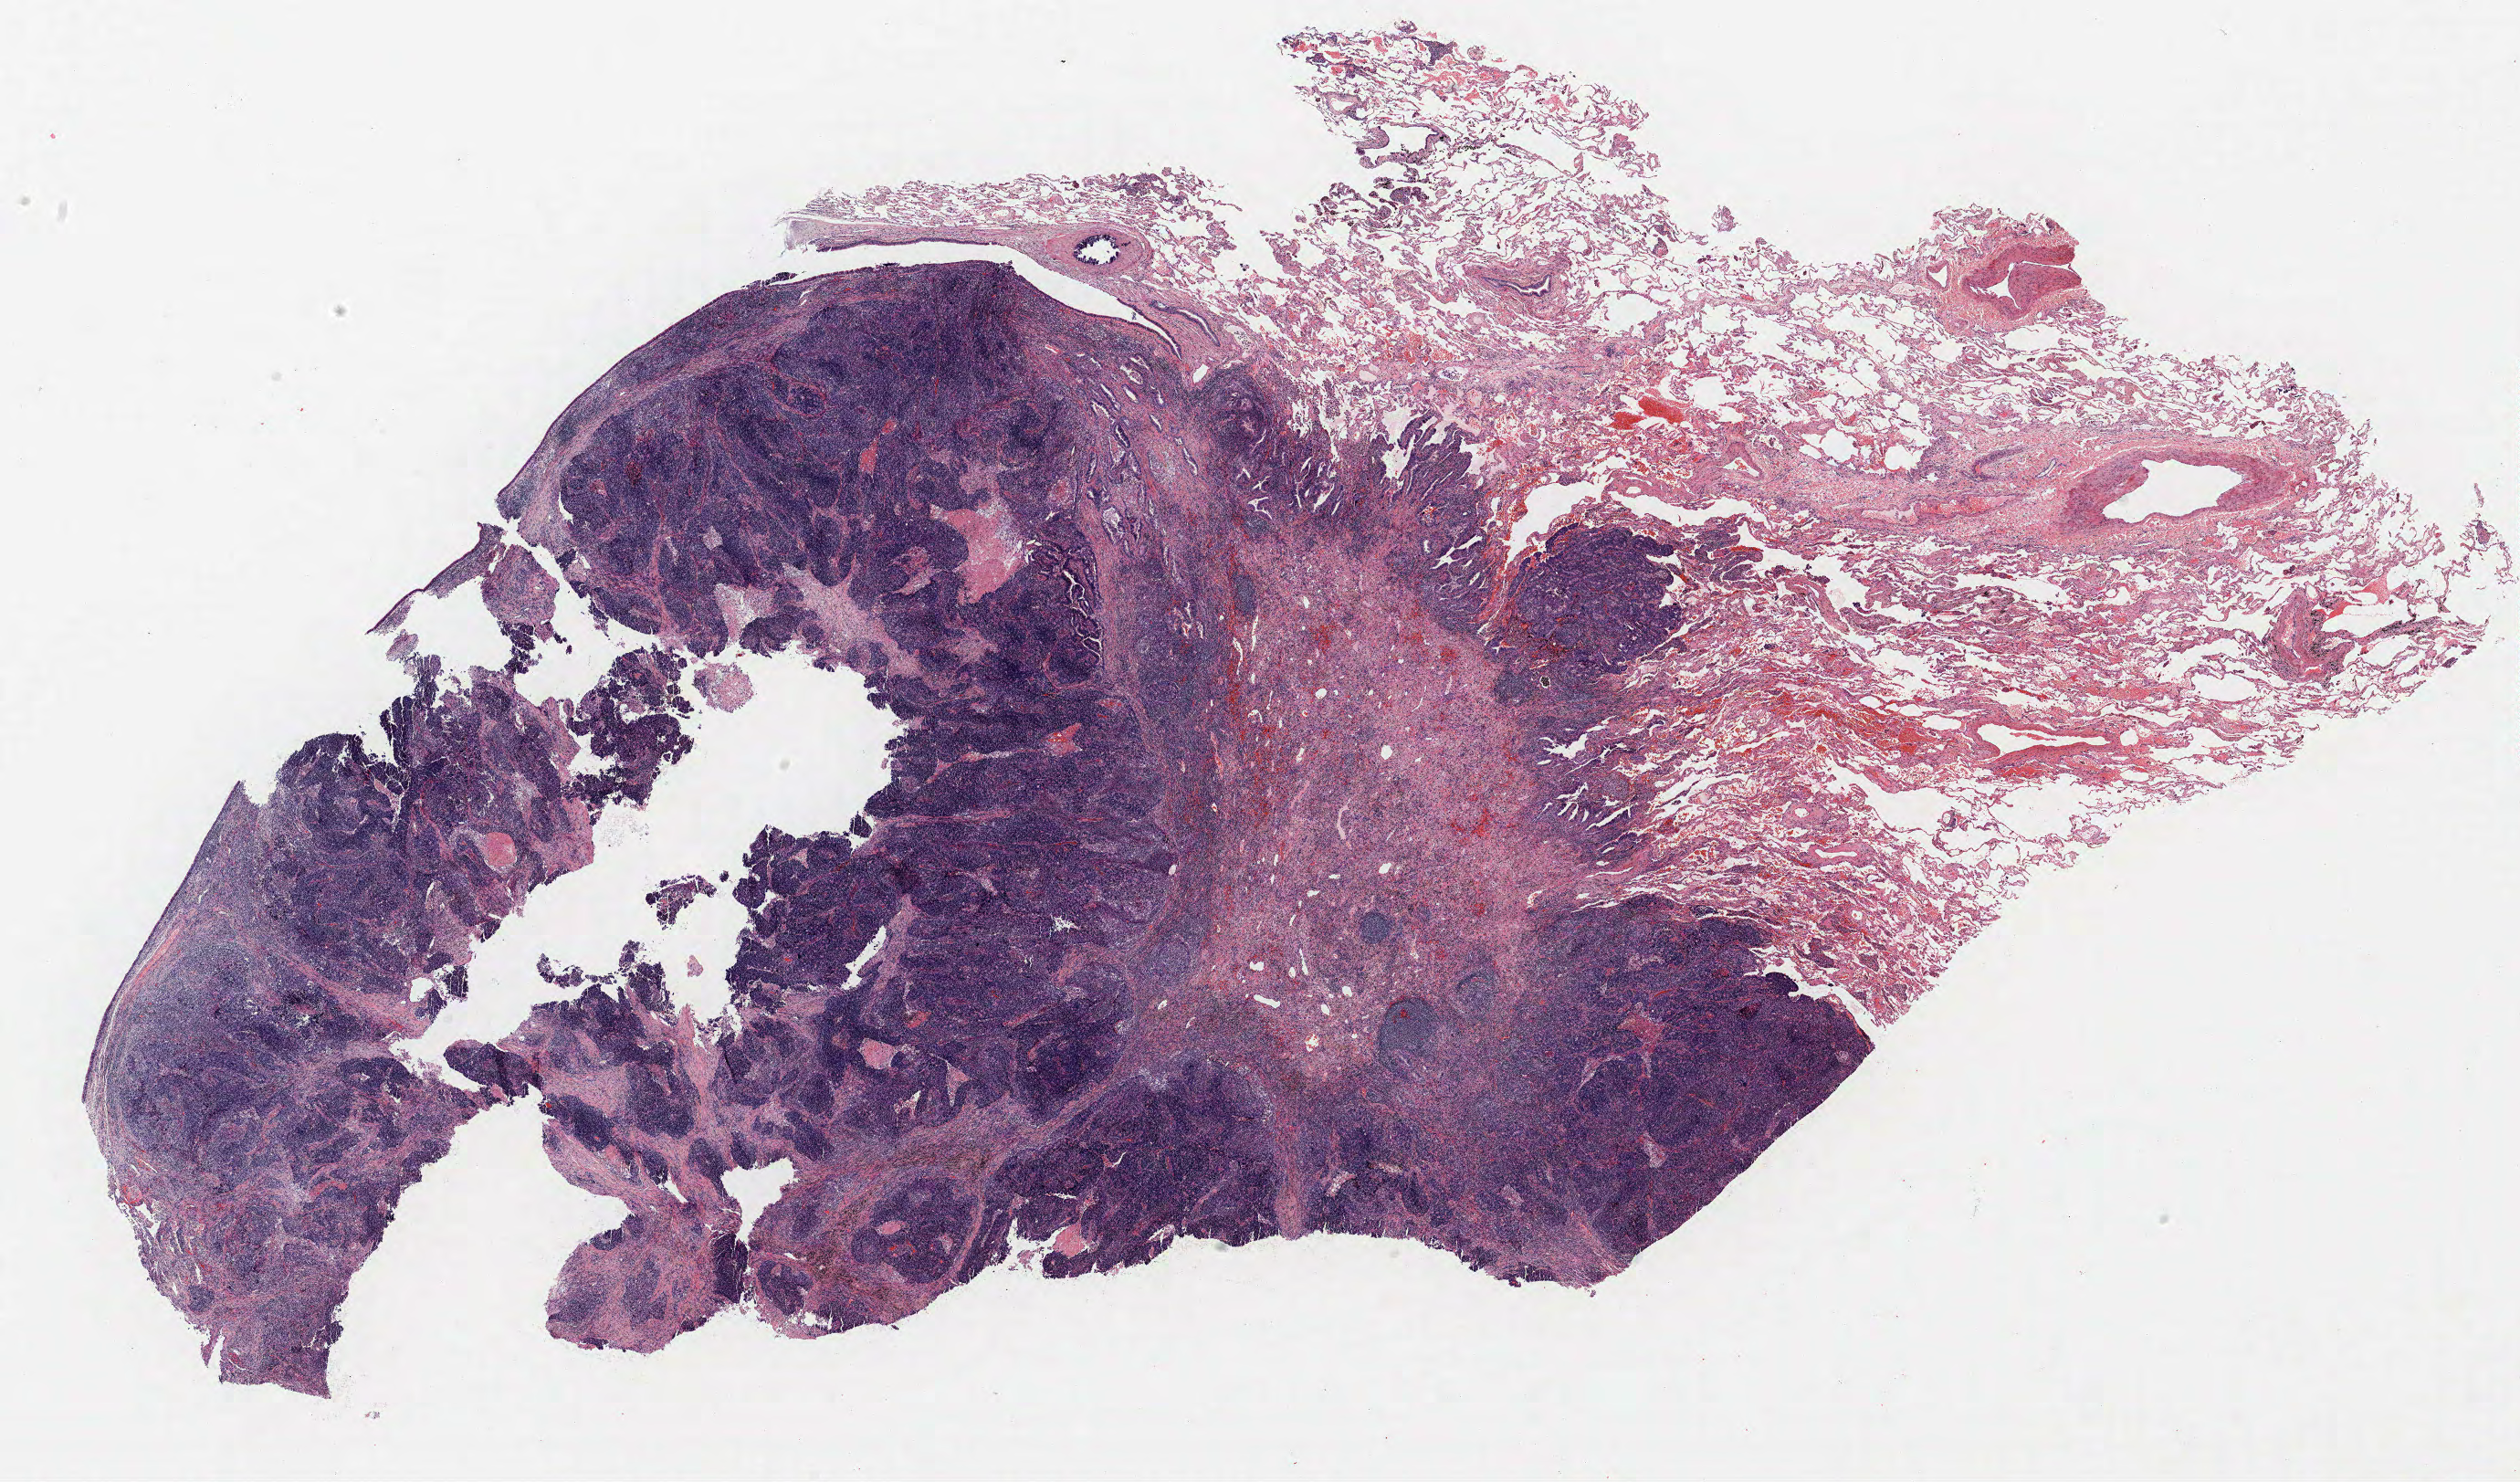
Hematoxylin and eosin (H&E) stained whole-slide image — low-resolution overview of the scanned area, about 22.1 x 13.0 mm, formalin-fixed paraffin-embedded (FFPE) section, lung tissue. Male, age 67 at enrolment. Current smoker at enrolment. Grade: poorly differentiated (G3).
Participant's lung-cancer diagnosis: Adenocarcinoma, NOS (ICD-O-3 8140/3). ICD-O-3 topography: upper lobe of lung (C34.1). Tumour size (pathology): 18 mm. Stage (AJCC 6th edition): IIA. Primary tumour location (clinical record): left upper lobe, left lower lobe.